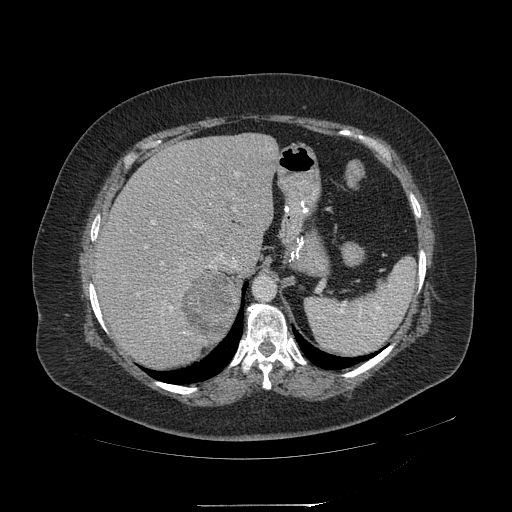
Contrast-enhanced abdominal CT, one axial slice; reconstruction kernel STANDARD; soft-tissue window (W 400 / L 40 HU); 1.25 mm slice thickness; 512 × 512 image matrix, field of view 453 × 453 mm. Female patient, age 55 years. Case-level facts recorded for this patient, not image findings: diagnosis: adrenocortical carcinoma; tumour side: right adrenal; tumour size at pathology: 11 cm; Ki-67 index: 20 %; stage (as recorded): 2.
Outlined on this slice (semi-automatically segmented with operator editing):
- mass: bounding box (x1, y1, x2, y2) in pixels: (181, 271, 235, 336)